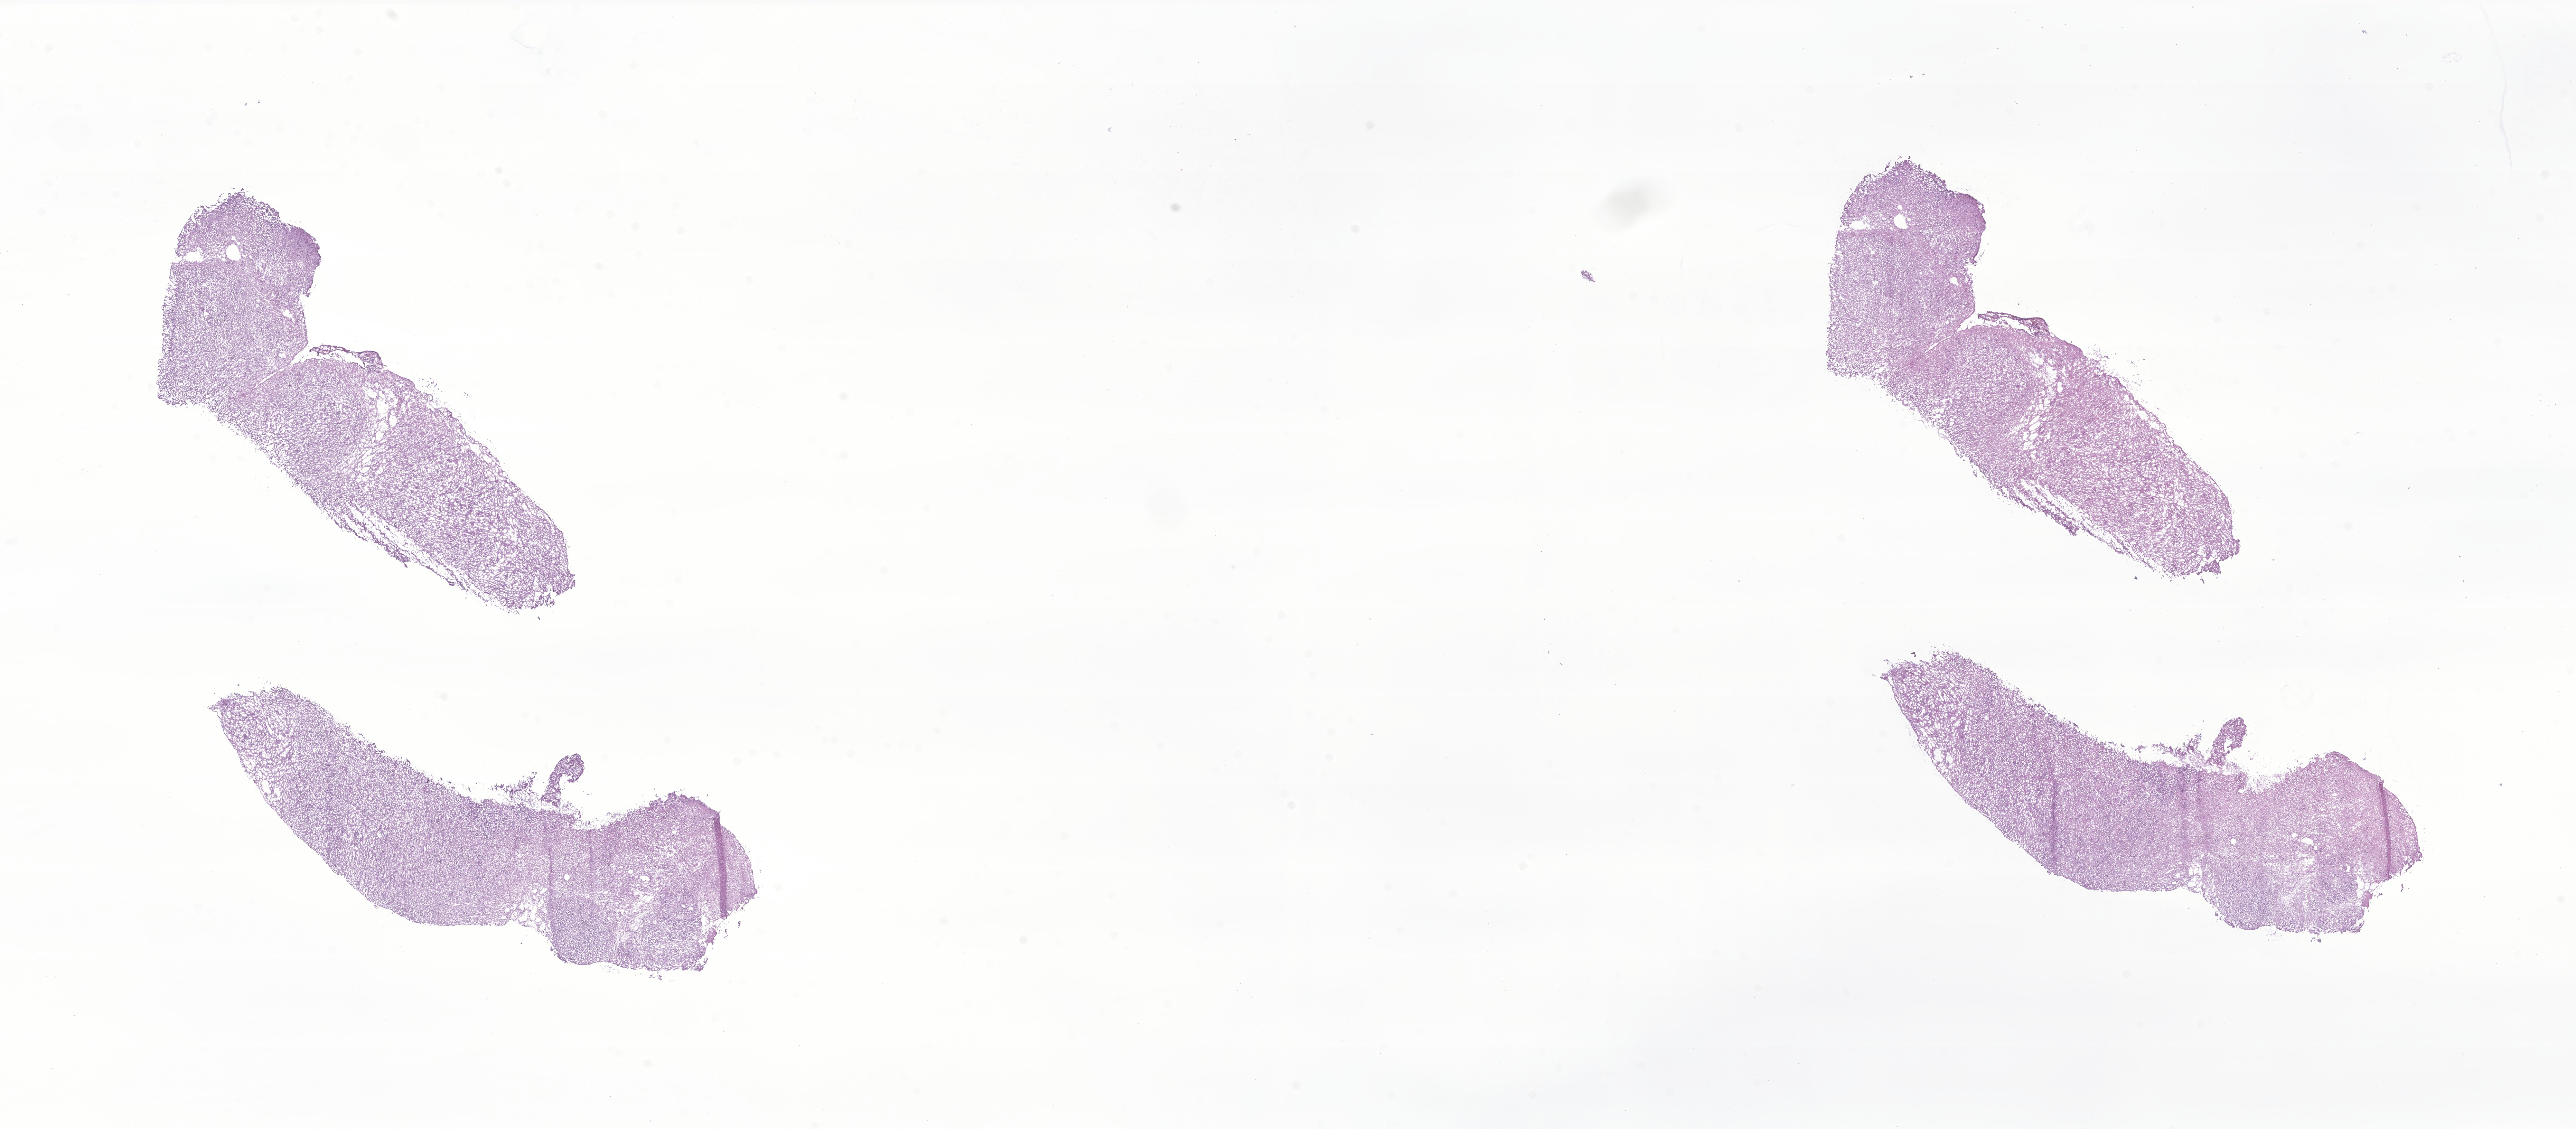
Whole-slide image, H&E stain of tumor tissue from the brain — whole scanned area (about 31.4 x 13.8 mm) shown as a low-resolution overview, frozen section. Male patient, age 807 days.
Recorded diagnosis: Neoplasm, uncertain whether benign or malignant.